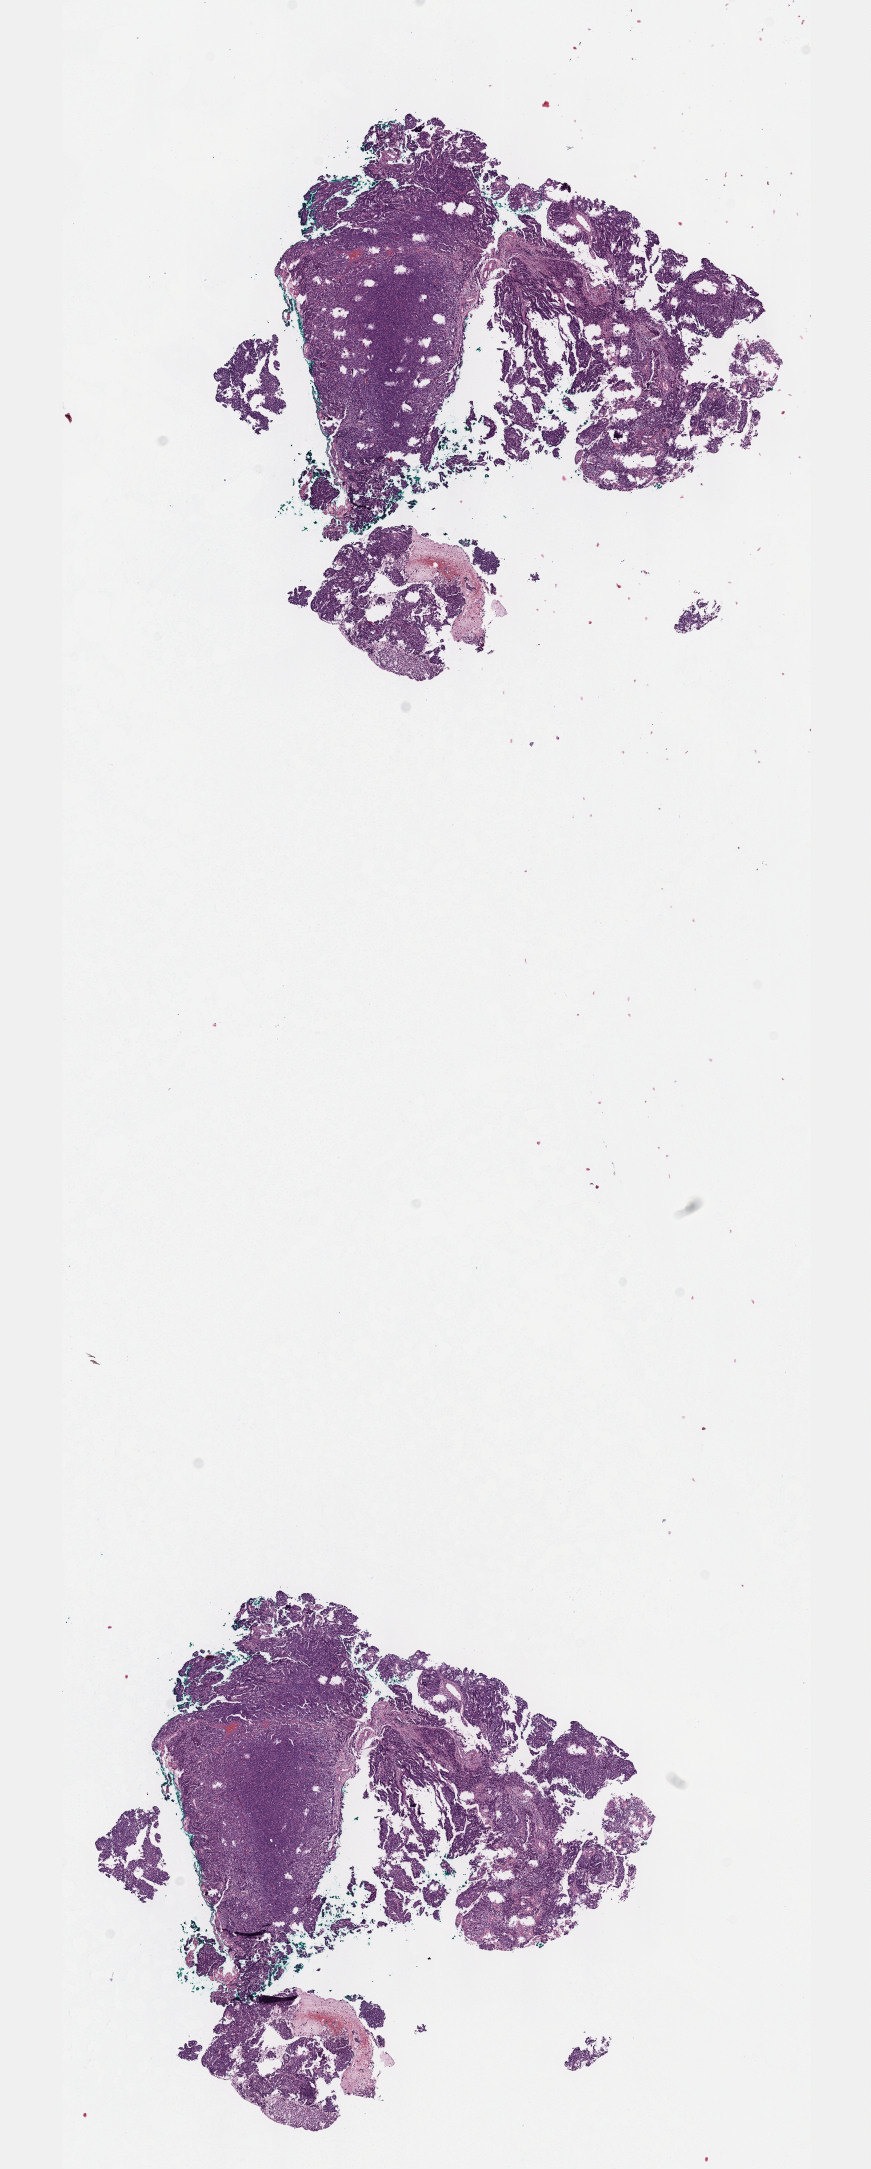
Hematoxylin and eosin (H&E) stained whole-slide image, whole scanned area (about 7.0 x 17.5 mm) shown as a low-resolution overview. FFPE section. Cervix, primary tumour sample. Patient: female, age at initial diagnosis 60 years. Histologic grade: G3 (poorly differentiated).
* diagnosis: Squamous cell carcinoma, NOS (cervix uteri)
* FIGO stage: IIB